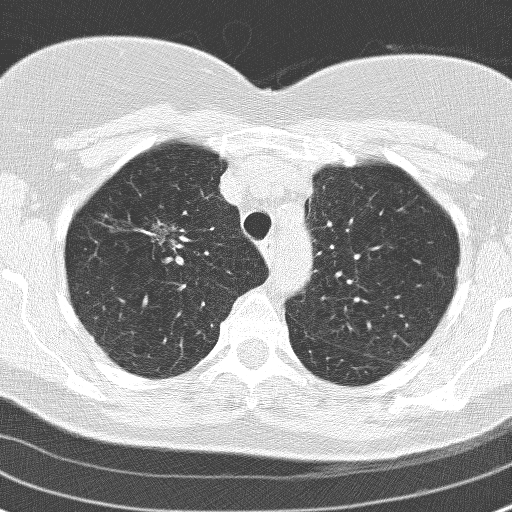
Axial slice from a low-dose chest CT screening exam; second annual screen; lung window (W 1500 / L -600 HU); 3.2 mm slice thickness; lung (sharp) reconstruction kernel (D). Female, age 60 years at enrolment. Former smoker at enrolment.
• Expert-annotated lung lesion, bounding box <123,209,179,257> (left, top, right, bottom; pixels).
• Screening reader's record for this exam (one nodule recorded; not confirmed to be the boxed lesion): non-calcified nodule or mass ≥4 mm, right upper lobe, 17 × 15 mm, spiculated (stellate) margins, soft tissue attenuation, pre-existing on the prior screen: yes; interval growth: yes.
• Official screen result: positive, other.
• Participant outcome: lung cancer diagnosed 78 days after this screen — adenocarcinoma, NOS, right upper lobe, moderately differentiated (G2), stage IA (AJCC 6th edition), 23 mm at pathology.